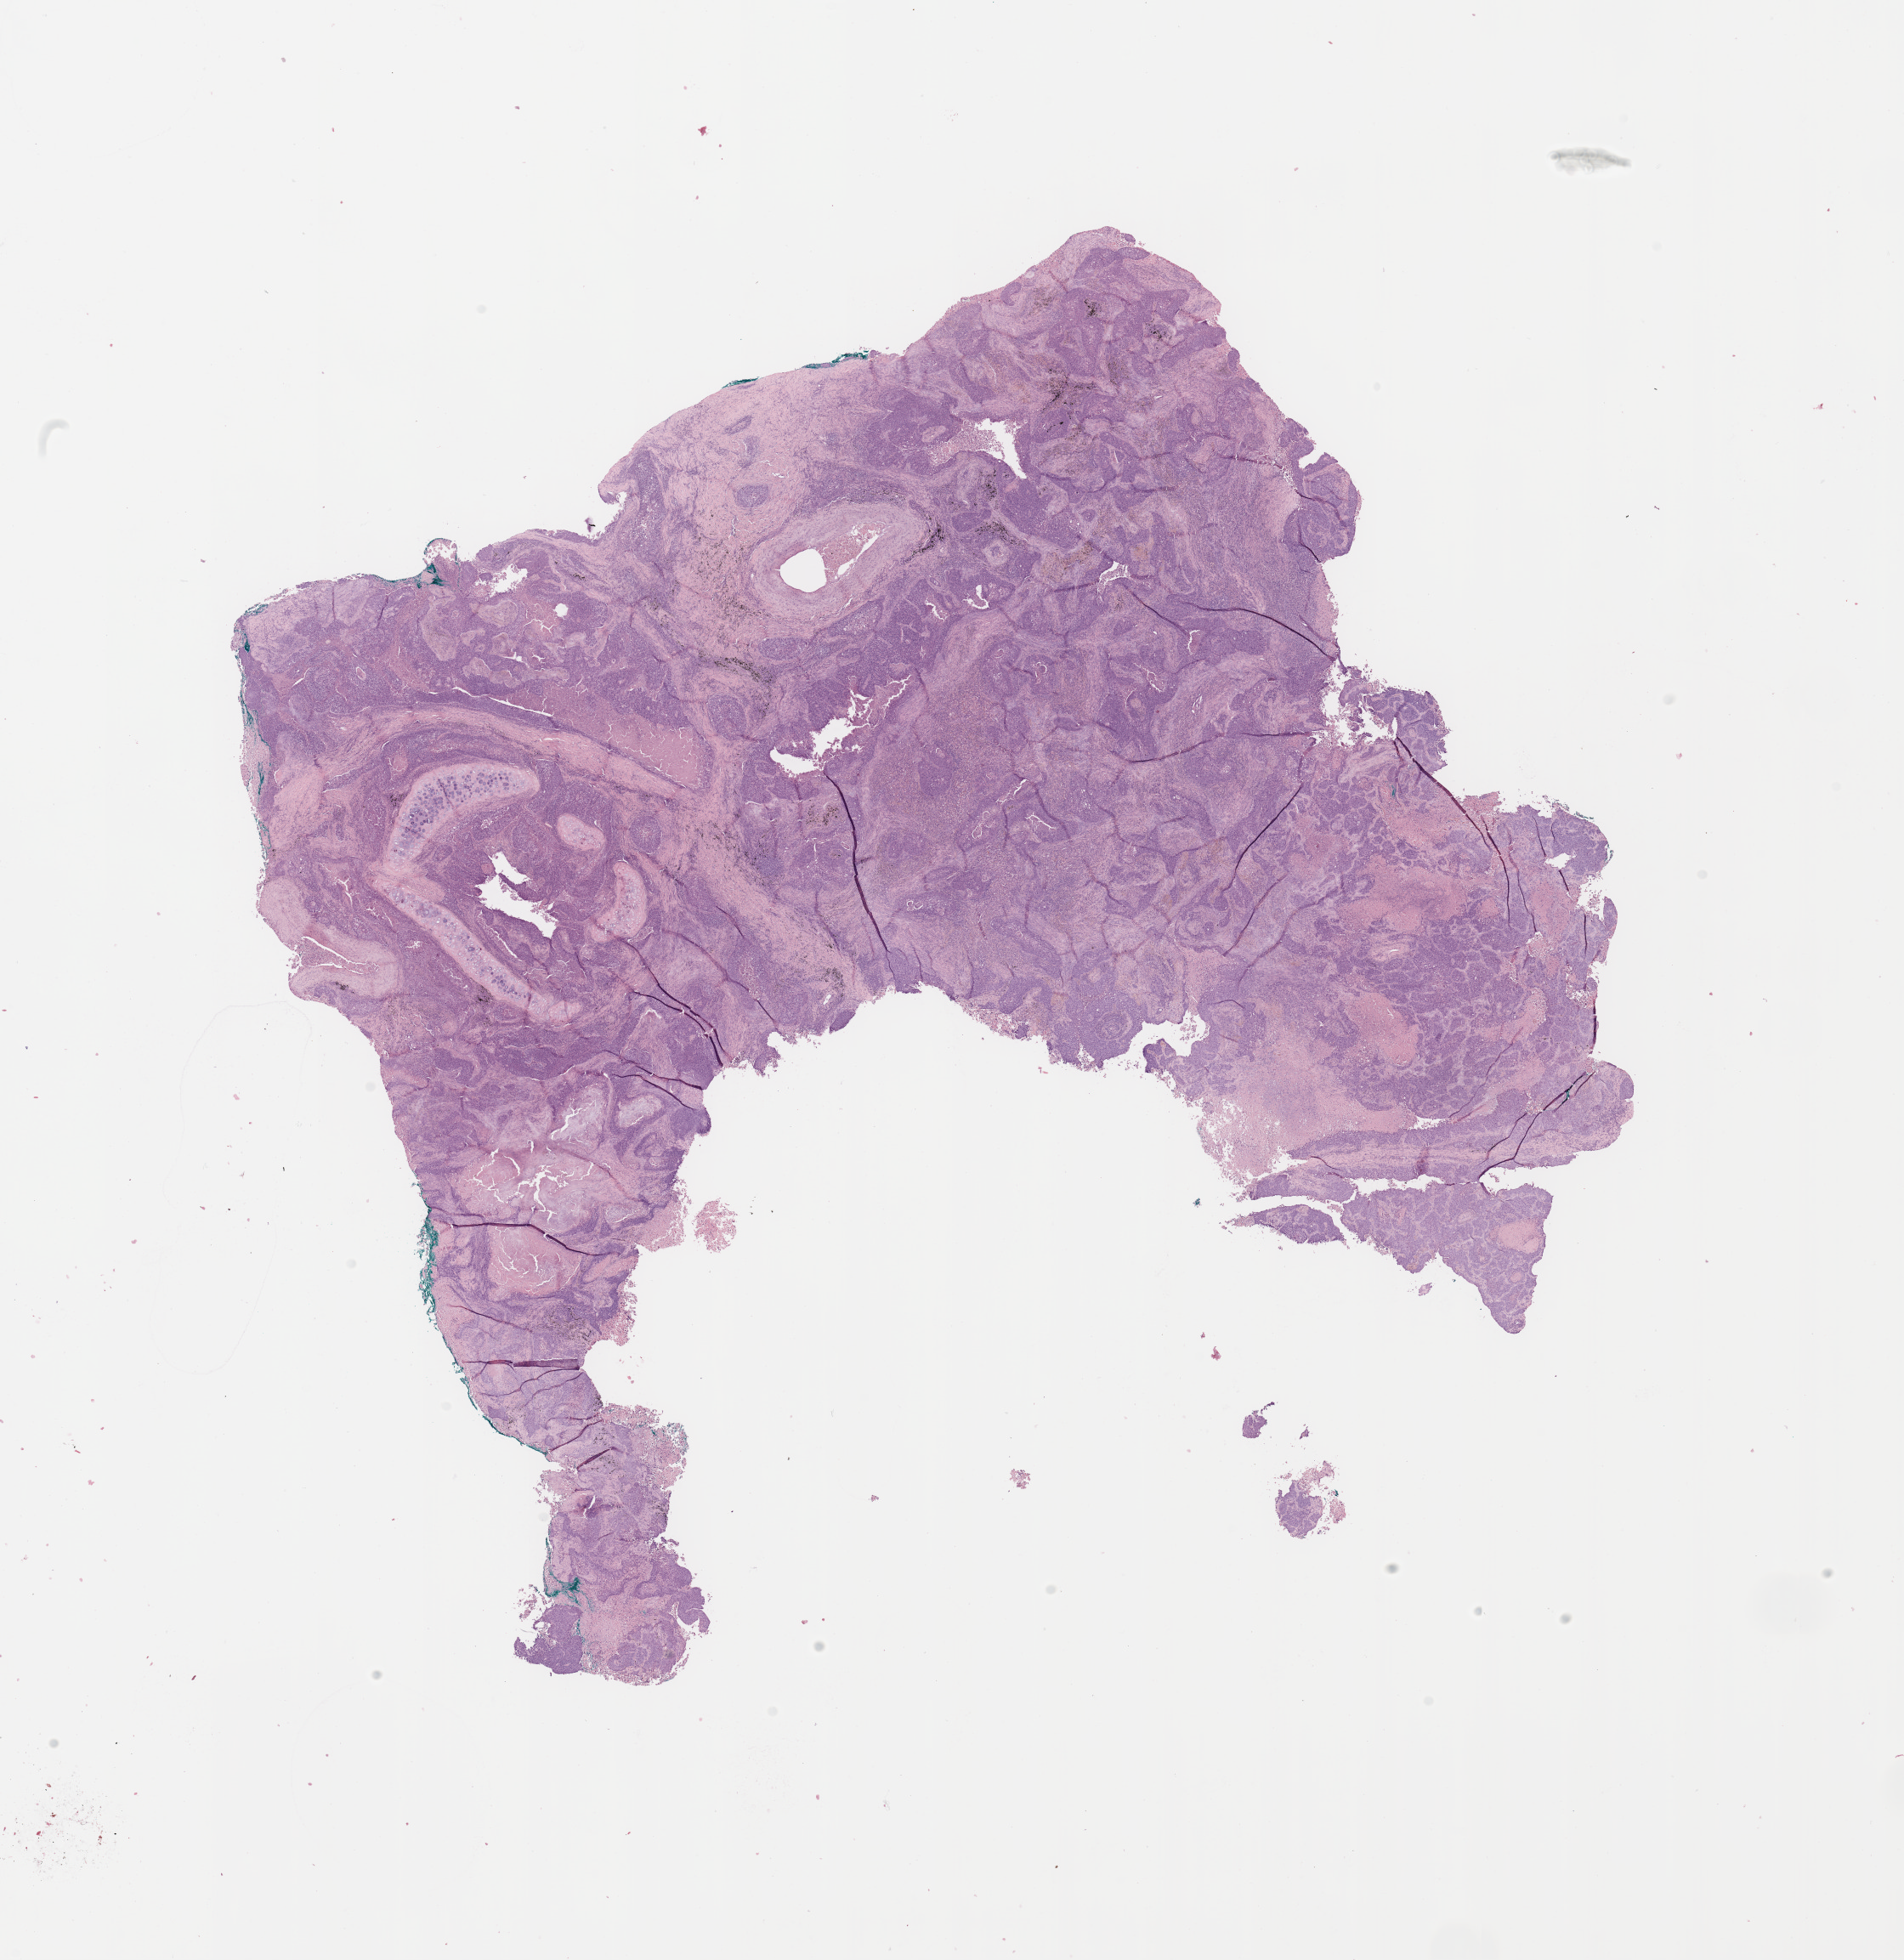
Digitized Hematoxylin and eosin (H&E) stained tissue section (whole slide) — whole scanned area (about 17.7 x 18.2 mm) shown as a low-resolution overview. Lung, tumour tissue. 75-year-old male patient. Histologic grade: G2 (moderately differentiated).
Primary tumour site (as recorded): right lower lobe. Diagnosis: Squamous cell carcinoma, NOS. AJCC pathologic stage: IIIA.